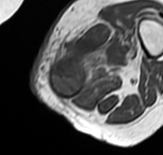
MRI of an extremity soft-tissue mass, one axial slice. MR volume resampled by the dataset authors to the PET/CT grid (not the native acquisition matrix). 3.27 mm slice thickness. 163 × 155 image matrix, field of view 159 × 151 mm. Female patient. From the clinical record (not read from this slice): histological type: pleomorphic leiomyosarcoma; grade: high; site of the primary tumour: left thigh.
Annotated regions visible in this slice (expert contour drawn on MRI and transferred to this co-registered scan by the dataset authors):
- gross tumour volume including surrounding oedema: bounding box [x1, y1, x2, y2] px = [49, 26, 136, 100]
- gross tumour volume (mass): [51, 58, 86, 98]